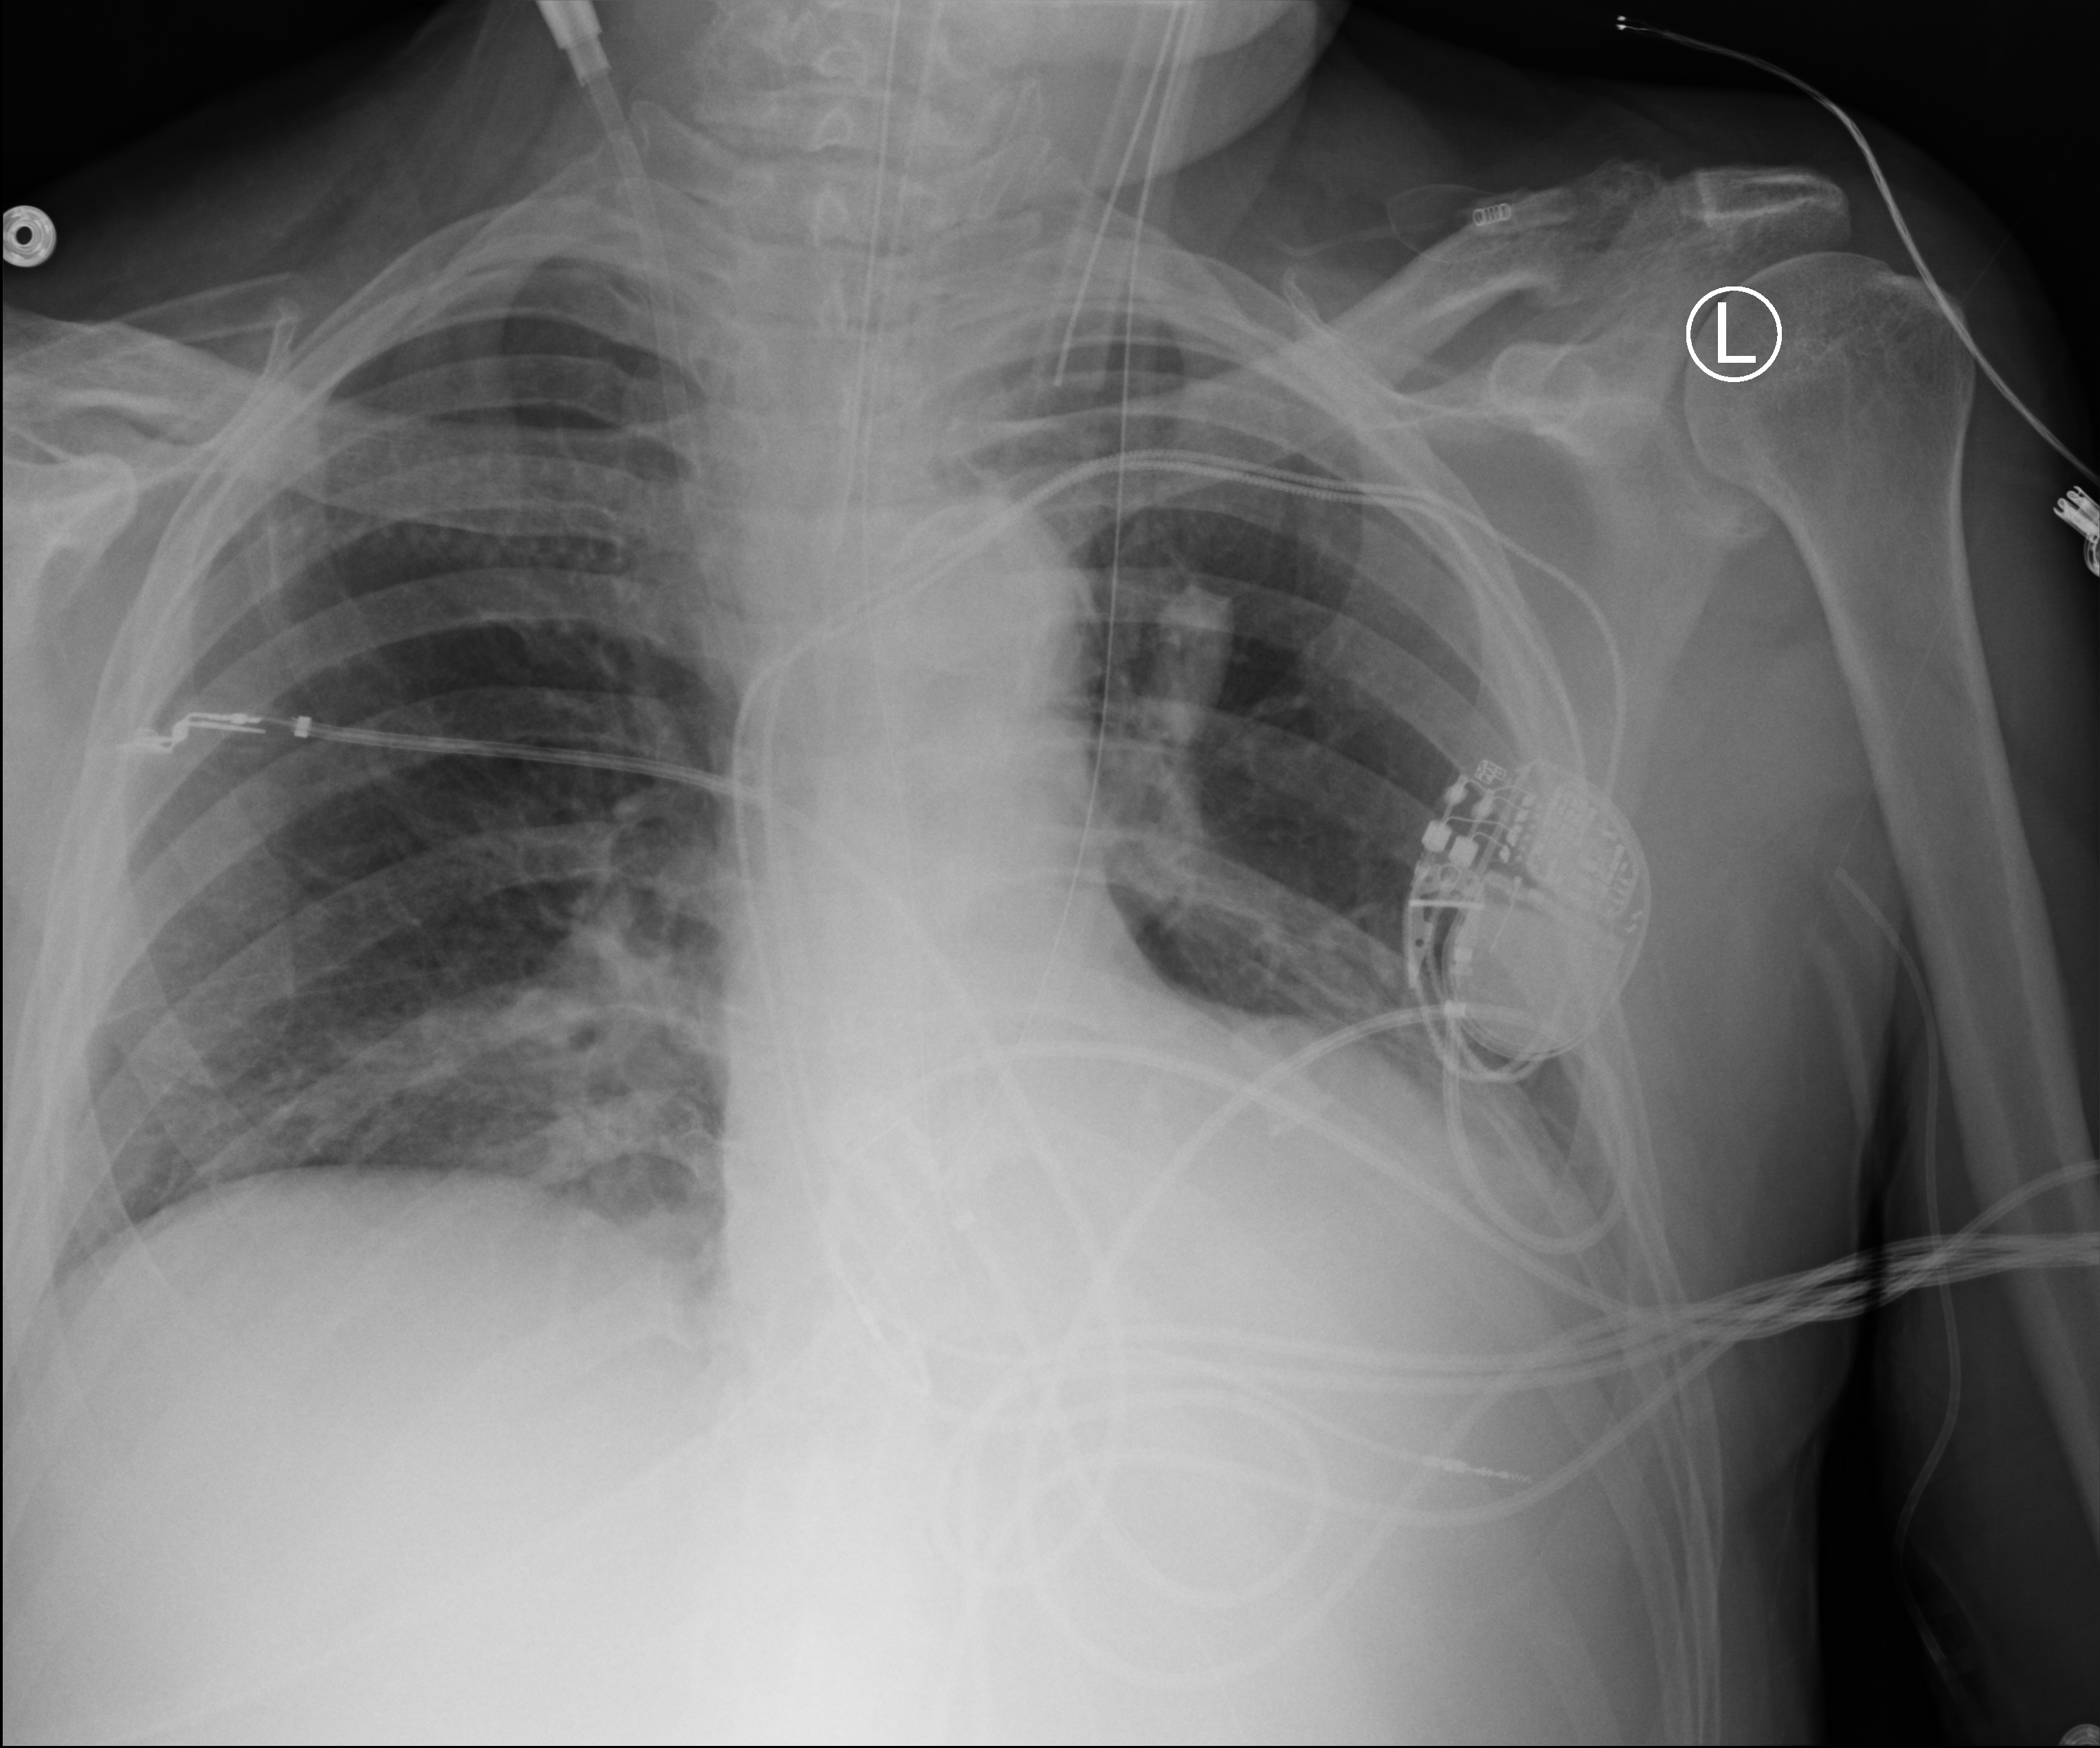
Portable chest radiograph; anteroposterior (AP) projection. Patient hospitalised with COVID-19; male, aged 60–74 years.
Hospital-stay facts (about this admission, not read from this image; timing relative to this image not recorded): admitted to intensive care during this hospital stay: yes.